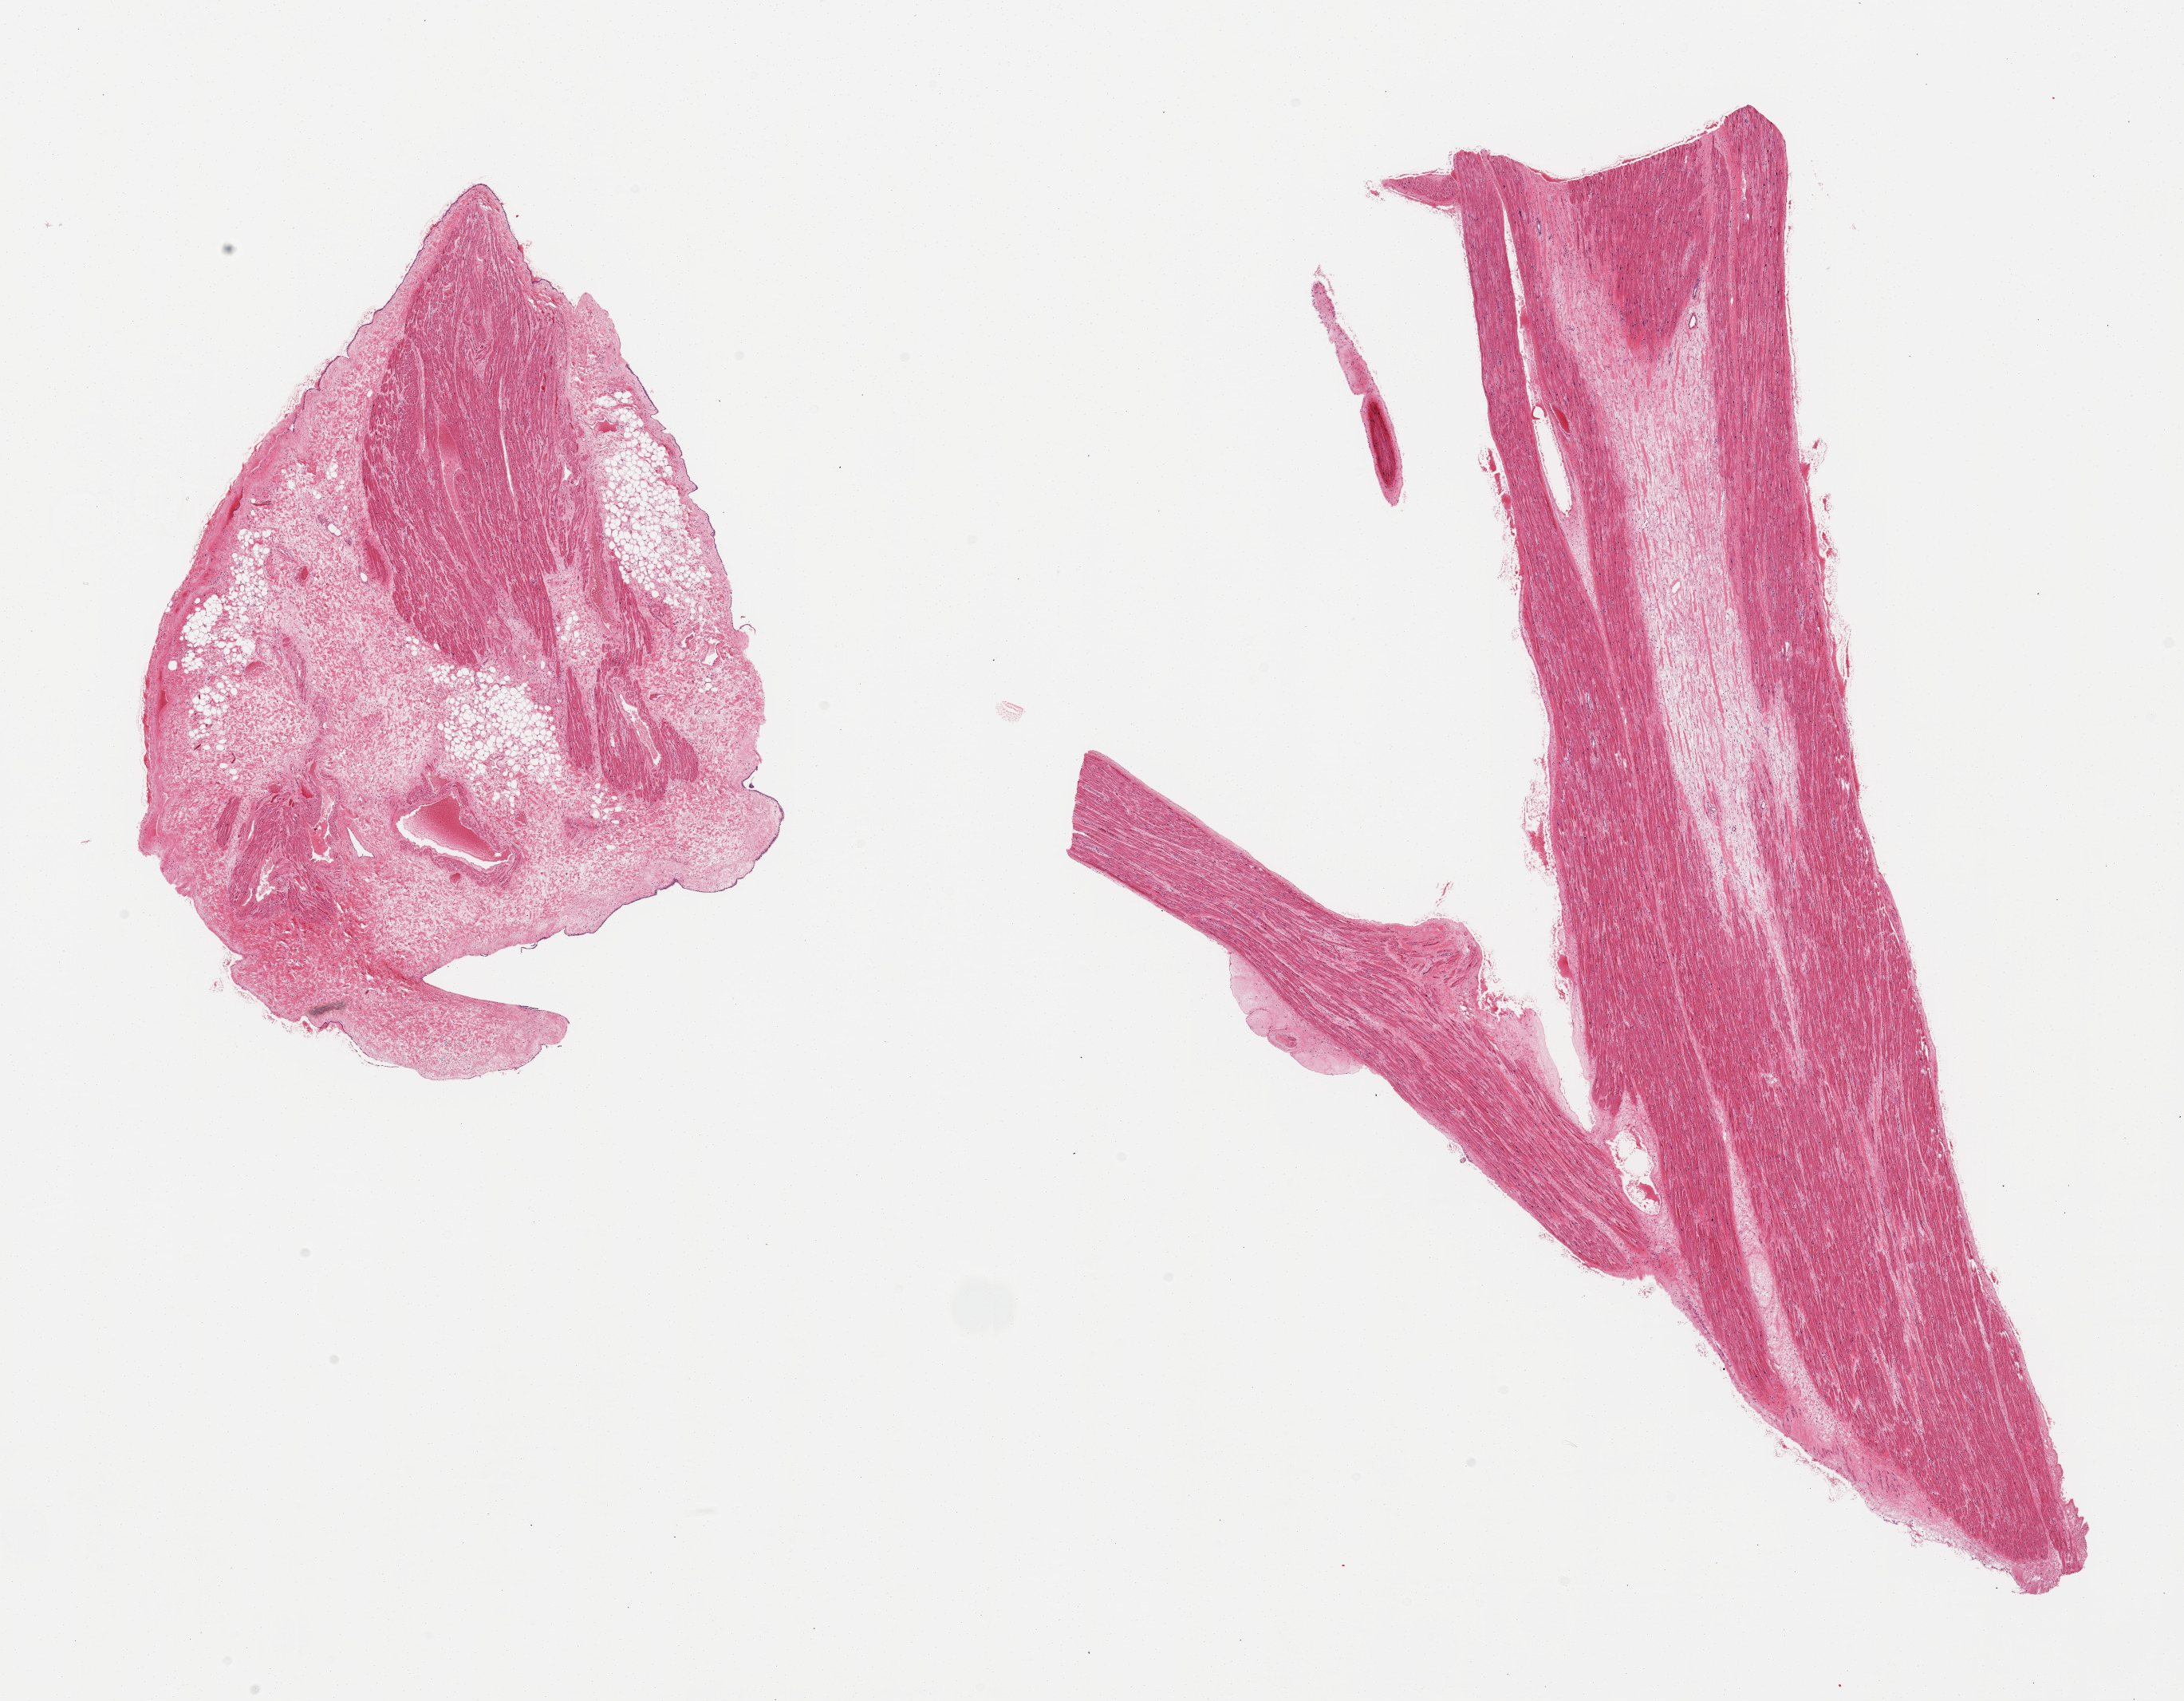
Whole-slide image, H&E stain, shown as a low-resolution overview of the whole scanned area (about 21.7 x 16.9 mm), PAXgene-fixed, paraffin-embedded tissue, sampled site (target tissue): auricular appendage, tissue donor sample. Donor: male.
• pathologist's review note for this sample: 2 pieces; 1 has 60% fat & fibrous stroma